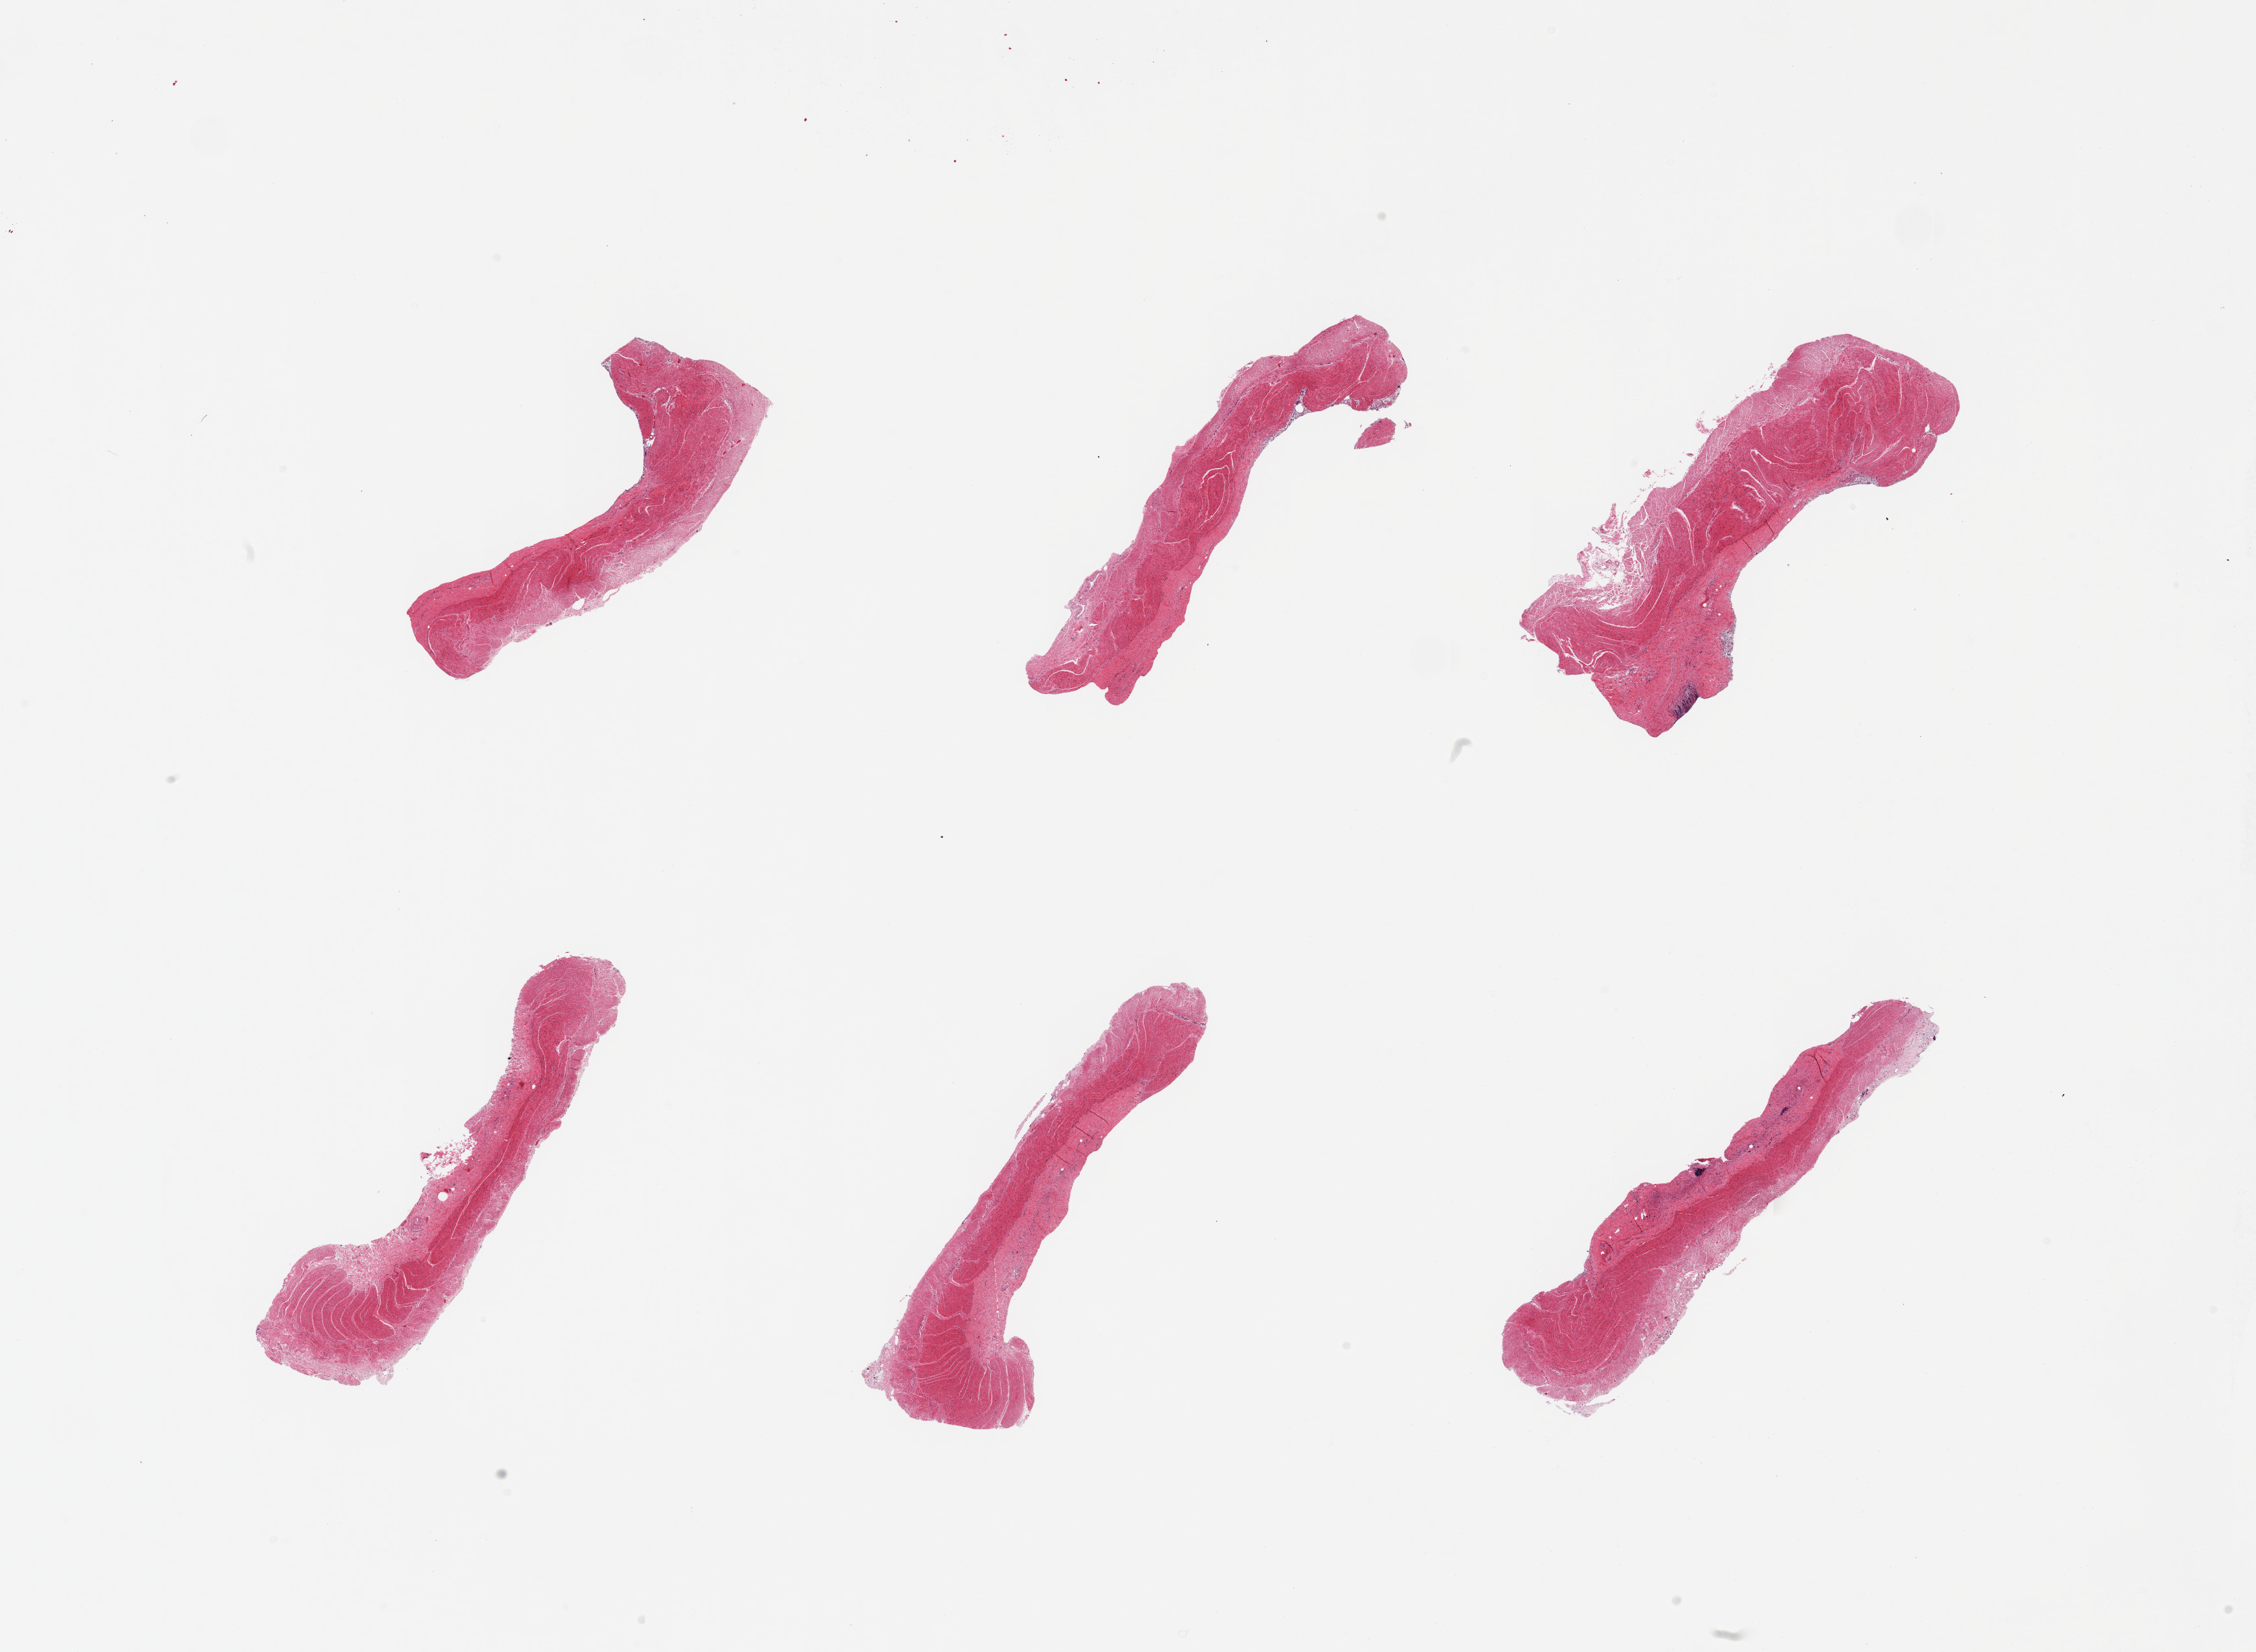
Whole-slide image, H&E stain, low-resolution overview of the scanned area, about 27.6 x 20.2 mm (slide scanned at 20x). PAXgene-fixed, paraffin-embedded tissue. Target tissue: sigmoid colon. Donor tissue sample. Female donor.
• pathologist's review note for this sample: 6 pieces, confirmed target muscularis